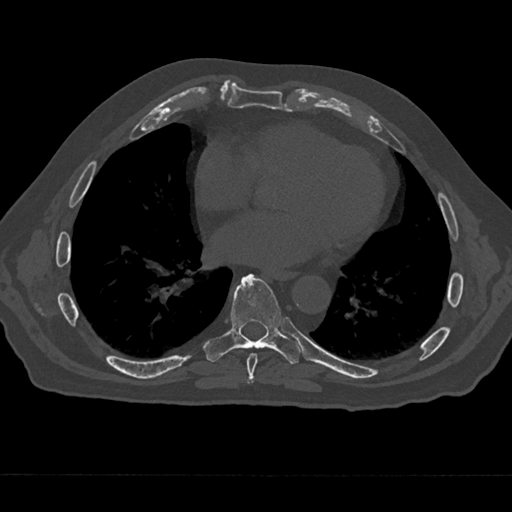
CT including the spine, one axial slice. Position 331 of 797 along the scan axis. 120 kVp. Bone window (W 1800 / L 400 HU). 0.5 mm slice thickness. 512 × 512 image matrix. Male patient, age 75 years. From the clinical record (not read from this slice): primary cancer: renal; vertebrae with lytic lesions (as recorded): T4.
Outlined on this slice (semi-automatic segmentation, software-assisted and operator-edited):
- T7 vertebra: bounding box (x1, y1, x2, y2) in pixels: (244, 353, 258, 382)
- T8 vertebra: (203, 273, 301, 364)